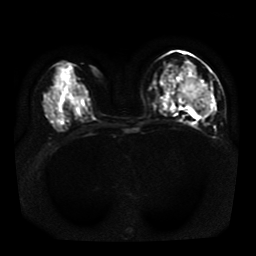
Breast MRI, one axial slice; position 21 of 41 along the scan axis; diffusion-weighted series; image 2 of 4 stored at this slice position (different b-values; order by instance number); 1.5 T; 5 mm slice thickness; 256 × 256 image matrix, field of view 330 × 330 mm. Female patient.
Structures marked on this image (manually delineated by an expert):
- tumour on diffusion-weighted imaging: bounding box (x1, y1, x2, y2) in pixels: (176, 79, 211, 116)